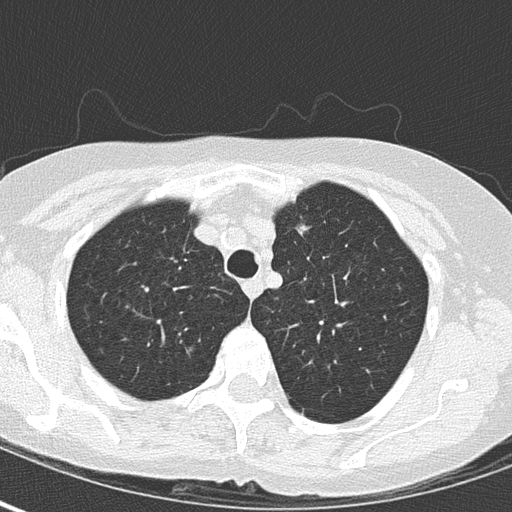
Chest CT (low-dose screening protocol), one axial image. Second annual screen. Lung window (W 1500 / L -600 HU). Slice 38 of 163 in the series. 512 × 512 image matrix, field of view 280 × 280 mm. Female participant, aged 64 years at enrolment.
Lesion marked by an expert reader, bounding box <277,209,329,255> (left, top, right, bottom; pixels). Screening reader's record for this exam (one nodule recorded; not confirmed to be the boxed lesion): non-calcified nodule or mass ≥4 mm, left upper lobe, 8 × 7 mm, pre-existing on the prior screen: yes. Participant outcome: lung cancer diagnosed 123 days after this screen — adenocarcinoma, NOS, left upper lobe, moderately differentiated (G2), stage IA (AJCC 6th edition), 7 mm at pathology.